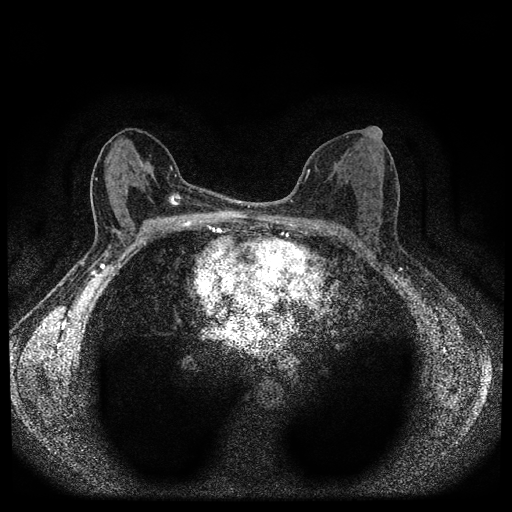
Breast MRI (dynamic contrast-enhanced, multi-phase), one axial slice; position 50 of 112 along the scan axis; dynamic contrast-enhanced series, time point 2 of 5 at this slice position (early post-contrast); 1.5 T; TE 2.7 ms, TR 5.4 ms; 2 mm slice thickness; 512 × 512 image matrix. Patient: female, 61 years.
Annotated regions visible in this slice (semi-automatic segmentation, software-assisted and operator-edited):
- breast lesion (labelled 'tumour' in the annotation; benign lesions carry a separate 'benign' label): bounding box [x1, y1, x2, y2] px = [169, 191, 182, 206]